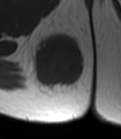
MRI of an extremity soft-tissue mass, one axial slice. Slice 20 of 47 in the series (ordered by position). MR volume resampled by the dataset authors to the PET/CT grid (not the native acquisition matrix). 121 × 139 image matrix, field of view 118 × 136 mm. Female patient. Case-level facts recorded for this patient, not image findings: histological type: epithelioid sarcoma; grade: intermediate; site of the primary tumour: right buttock.
Outlined on this slice (expert contour drawn on MRI and transferred to this co-registered scan by the dataset authors):
- gross tumour volume including surrounding oedema: bounding box (x1, y1, x2, y2) in pixels: (27, 30, 85, 97)
- gross tumour volume (mass): (32, 36, 83, 87)